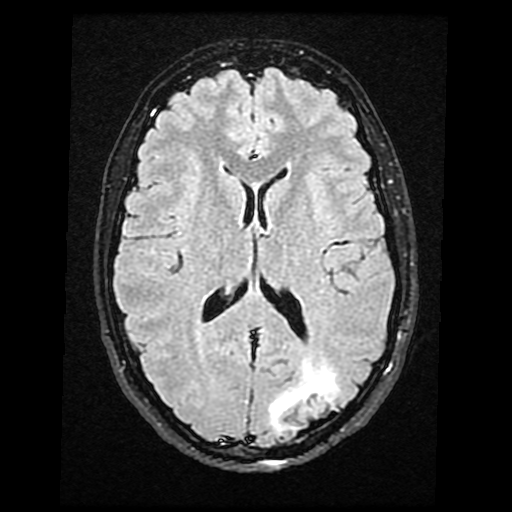
Brain MRI from a brain-tumour surgery series, one axial slice; slice 19 of 40 in the series (ordered by position); T2 FLAIR; 4 mm slice thickness; 512 × 512 image matrix, field of view 240 × 240 mm. Case-level facts recorded for this patient, not image findings: histopathology: Glioma with ependymal features; WHO grade: 2; tumour location: Left Parietal.
Structures marked on this image (manually delineated by an expert):
- tumour: bounding box [x1, y1, x2, y2] px = [268, 358, 340, 432]